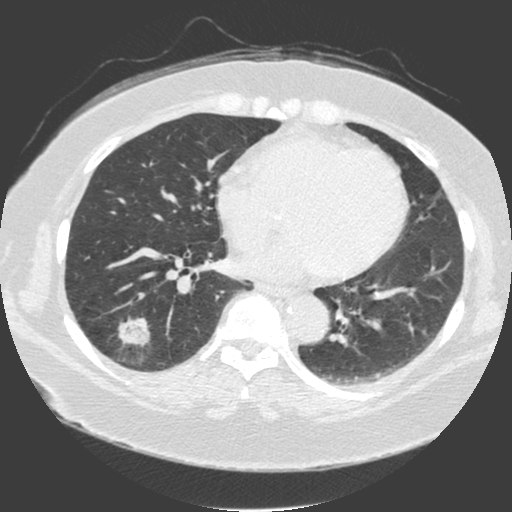
Axial slice from a low-dose chest CT screening exam. Third screening round (two years after baseline). Lung window (W 1500 / L -600 HU). Slice 99 of 175 in the series. Female, age 56 years at enrolment.
Lesion marked by an expert reader, bounding box [x1, y1, x2, y2] px = [105, 304, 157, 353]. The screening reader recorded 4 non-calcified nodules or masses ≥4 mm on this exam (left lower lobe, right lower lobe, right lower lobe, right lower lobe); which of them this box marks is not recorded. Official screen result: positive, other. Later outcome: lung cancer diagnosed 20 days after this screen — adenosquamous carcinoma, right lower lobe, poorly differentiated (G3), stage IA (AJCC 6th edition), 25 mm at pathology.